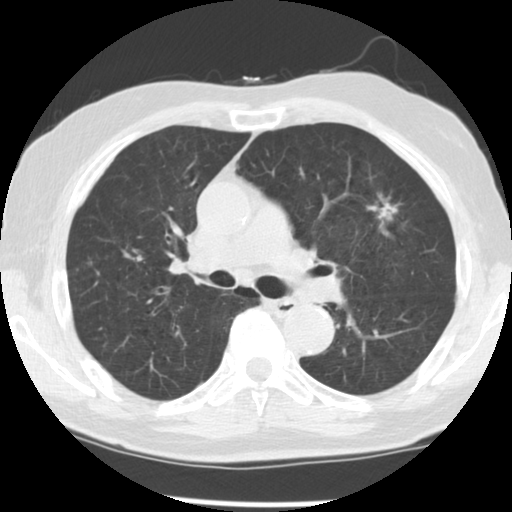
Low-dose screening chest CT, one axial slice; slice 79 of 131 in the series (ordered by position); 140 kVp; lung window (W 1500 / L -600 HU); 2.5 mm slice thickness; 512 × 512 image matrix, field of view 330 × 330 mm.
Outlined on this slice (expert manual segmentation):
- lesion 1 (tumor, upper lobe of left lung): bounding box [x1, y1, x2, y2] px = [368, 195, 398, 221]